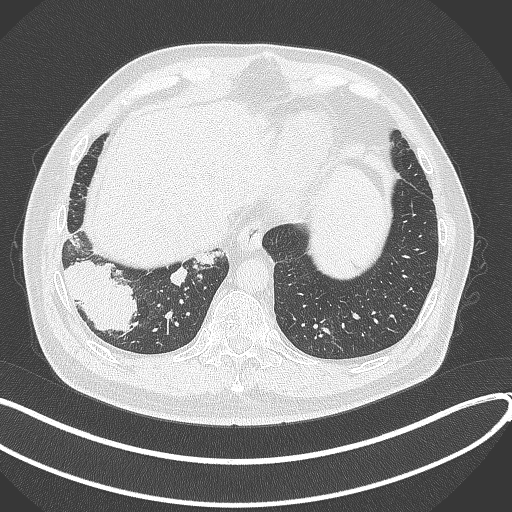
Chest CT, one axial slice. Position 70 of 360 along the scan axis. Reconstruction kernel B70f. Lung window (W 1500 / L -600 HU). 1 mm slice thickness. 512 × 512 image matrix, field of view 400 × 400 mm. Male patient, age 59 years.
Annotated regions visible in this slice (bounding box drawn by a radiologist):
- lung tumour (recorded histology: adenocarcinoma): box from (x=63, y=254) to (x=140, y=337) px